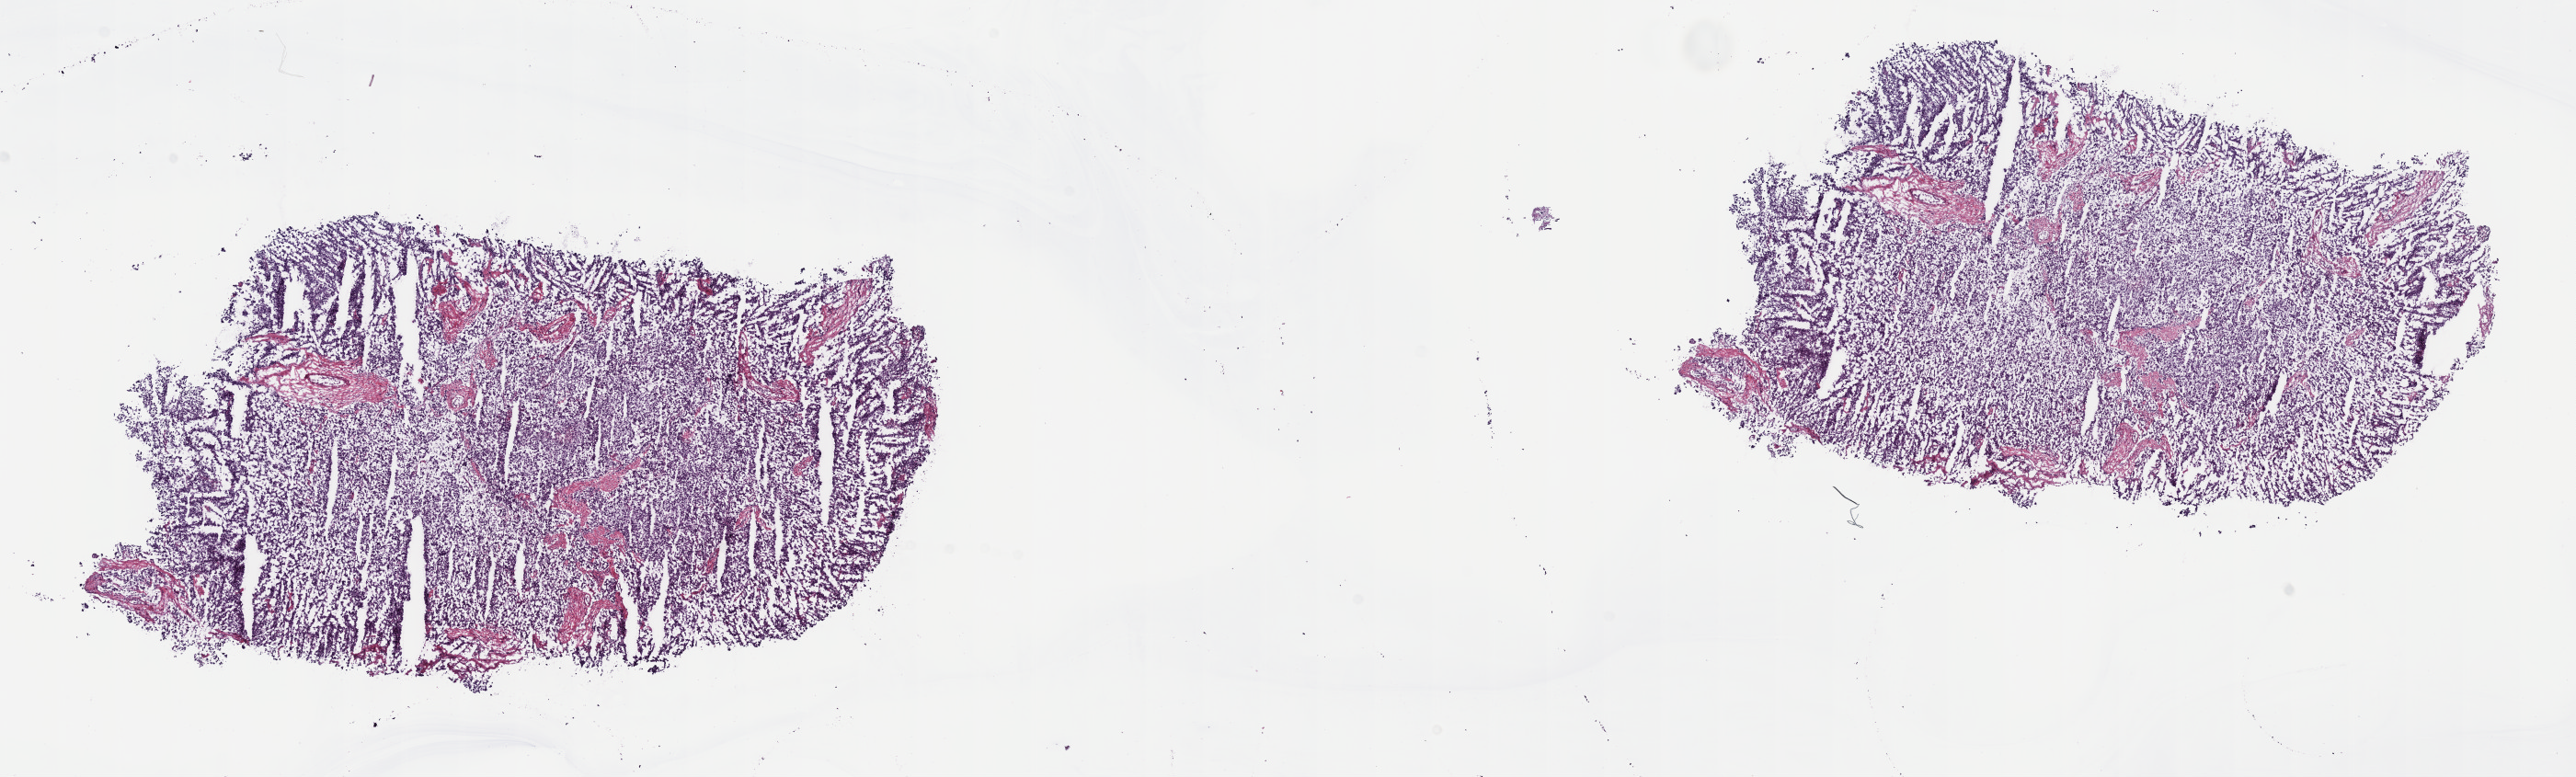
Digitized Hematoxylin and eosin (H&E) stained tissue section (whole slide), shown as a low-resolution overview of the whole scanned area (about 22.7 x 6.8 mm, slide scanned at 40x). Frozen section from the top of the tissue portion. Testis, primary tumour sample. Male, age 31 years at initial diagnosis. Slide review estimates, as recorded: tumour cells 100%, tumour nuclei 90%, normal cells 0%, stromal cells 0%, necrosis 0%. Infiltration values recorded for this section: lymphocyte infiltration 0%, monocyte infiltration 0%, neutrophil infiltration 0%.
Pathologic diagnosis: Seminoma, NOS. AJCC pathologic stage: IS (5th edition).